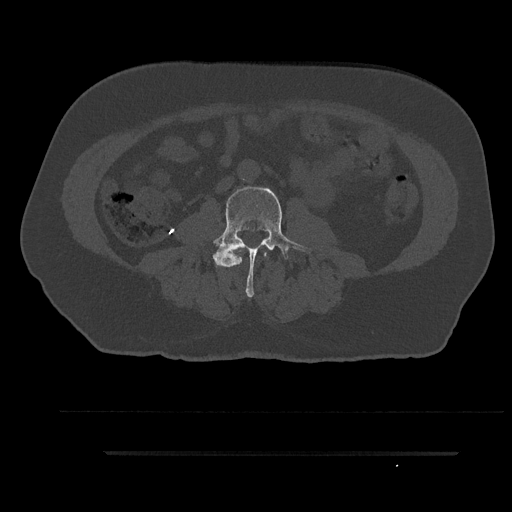
CT including the spine, one axial slice; slice 42 of 797 in the series (ordered by position); 120 kVp; bone window (W 1800 / L 400 HU); 512 × 512 image matrix, field of view 432 × 432 mm. Male patient, age 63 years. From the clinical record (not read from this slice): primary cancer: renal.
Outlined on this slice (semi-automatic segmentation, software-assisted and operator-edited):
- L2 vertebra: bounding box [x1, y1, x2, y2] px = [235, 250, 267, 265]
- L3 vertebra: [200, 185, 312, 297]